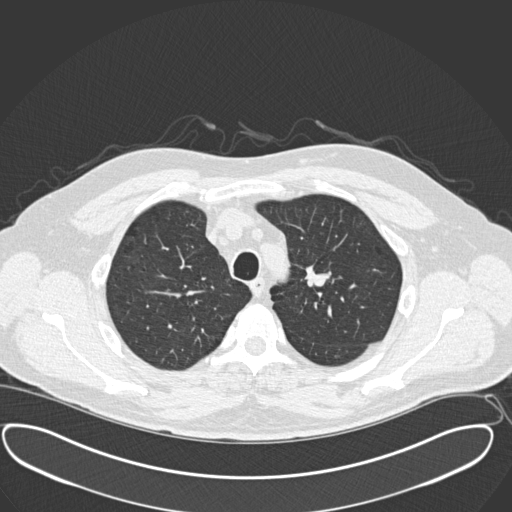
Low-dose screening chest CT, axial slice. Third annual screen. Lung window (W 1500 / L -600 HU). Standard (soft-tissue) reconstruction kernel (B30f). Slice 41 of 181 in the series. Male participant, aged 56 years at enrolment.
Expert reader's lesion annotation, bounding box [x1, y1, x2, y2] px = [291, 262, 343, 309]. No non-calcified nodule or mass ≥4 mm was recorded by the screening reader at this exam. Participant outcome: lung cancer diagnosed 156 days after this screen — neuroendocrine carcinoma, NOS, left upper lobe, well differentiated (G1), stage IA (AJCC 6th edition), 20 mm at pathology.